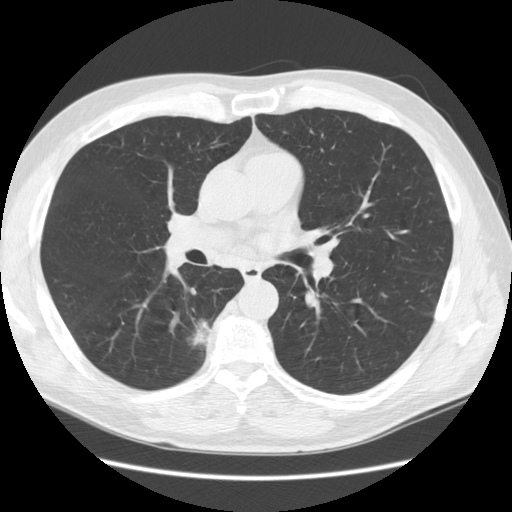
Low-dose screening chest CT, axial slice, second annual screen, lung window (W 1500 / L -600 HU), 2.5 mm slice thickness, standard (soft-tissue) reconstruction kernel (STANDARD), 120 kVp, slice 61 of 133 in the series, 512 × 512 image matrix, field of view 370 × 370 mm. Male participant, aged 69 years at enrolment.
Lesion marked by an expert reader, bounding box (x1, y1, x2, y2) in pixels: (169, 306, 229, 363). The screening reader recorded 2 non-calcified nodules or masses ≥4 mm on this exam; which of them this box marks is not recorded. Lung cancer was diagnosed 88 days after this screen: bronchiolo-alveolar adenocarcinoma, NOS, right lower lobe, well differentiated (G1), stage IB (AJCC 6th edition), 23 mm at pathology.